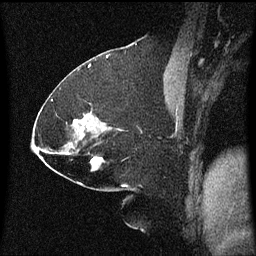
Breast MRI (dynamic contrast-enhanced), one sagittal slice; slice 31 of 60 in the series (ordered by position); dynamic contrast-enhanced series, image 2 of 3 at this slice position (ordered by acquisition); 1.5 T; TE 4.2 ms, TR 8 ms; 2.1 mm slice thickness; 256 × 256 image matrix, field of view 200 × 200 mm. Female patient, age 59 years.
Annotated regions visible in this slice (semi-automatic segmentation, software-assisted and operator-edited):
- analysis volume of interest (the breast-tissue region the enhancement analysis was run in; not a lesion): bounding box <88,152,105,171> (left, top, right, bottom; pixels)
- tumour enhancement mask (voxels above the 70 % enhancement threshold inside the analysis volume of interest): <92,158,99,171>